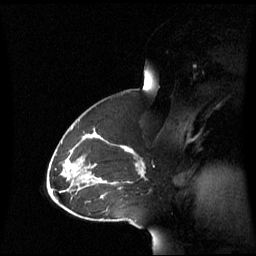
Breast MRI (dynamic contrast-enhanced), one sagittal slice. Position 39 of 60 along the scan axis. Dynamic contrast-enhanced series, image 2 of 3 at this slice position (ordered by acquisition). 1.5 T. TE 4.2 ms, TR 8.4 ms. 2.8 mm slice thickness. 256 × 256 image matrix, field of view 270 × 270 mm. Female patient, age 43 years. Case-level facts recorded for this patient, not image findings: setting: breast cancer imaged before/during neoadjuvant chemotherapy; receptor status: triple-negative.
Outlined on this slice (semi-automatically segmented with operator editing):
- analysis volume of interest (the breast-tissue region the enhancement analysis was run in; not a lesion): bounding box <69,137,143,198> (left, top, right, bottom; pixels)
- tumour enhancement mask (voxels above the 70 % enhancement threshold inside the analysis volume of interest): <122,146,143,177>